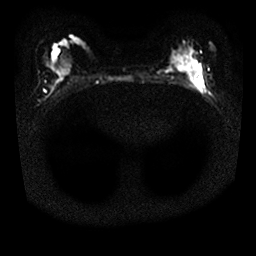
Breast MRI, one axial slice. Slice 14 of 25 in the series (ordered by position). Diffusion-weighted series; image 2 of 4 stored at this slice position (different b-values; order by instance number). 1.5 T. 4 mm slice thickness. 256 × 256 image matrix, field of view 310 × 310 mm. Female patient.
Outlined on this slice (expert manual segmentation):
- tumour on diffusion-weighted imaging: box from (x=192, y=76) to (x=207, y=93) px